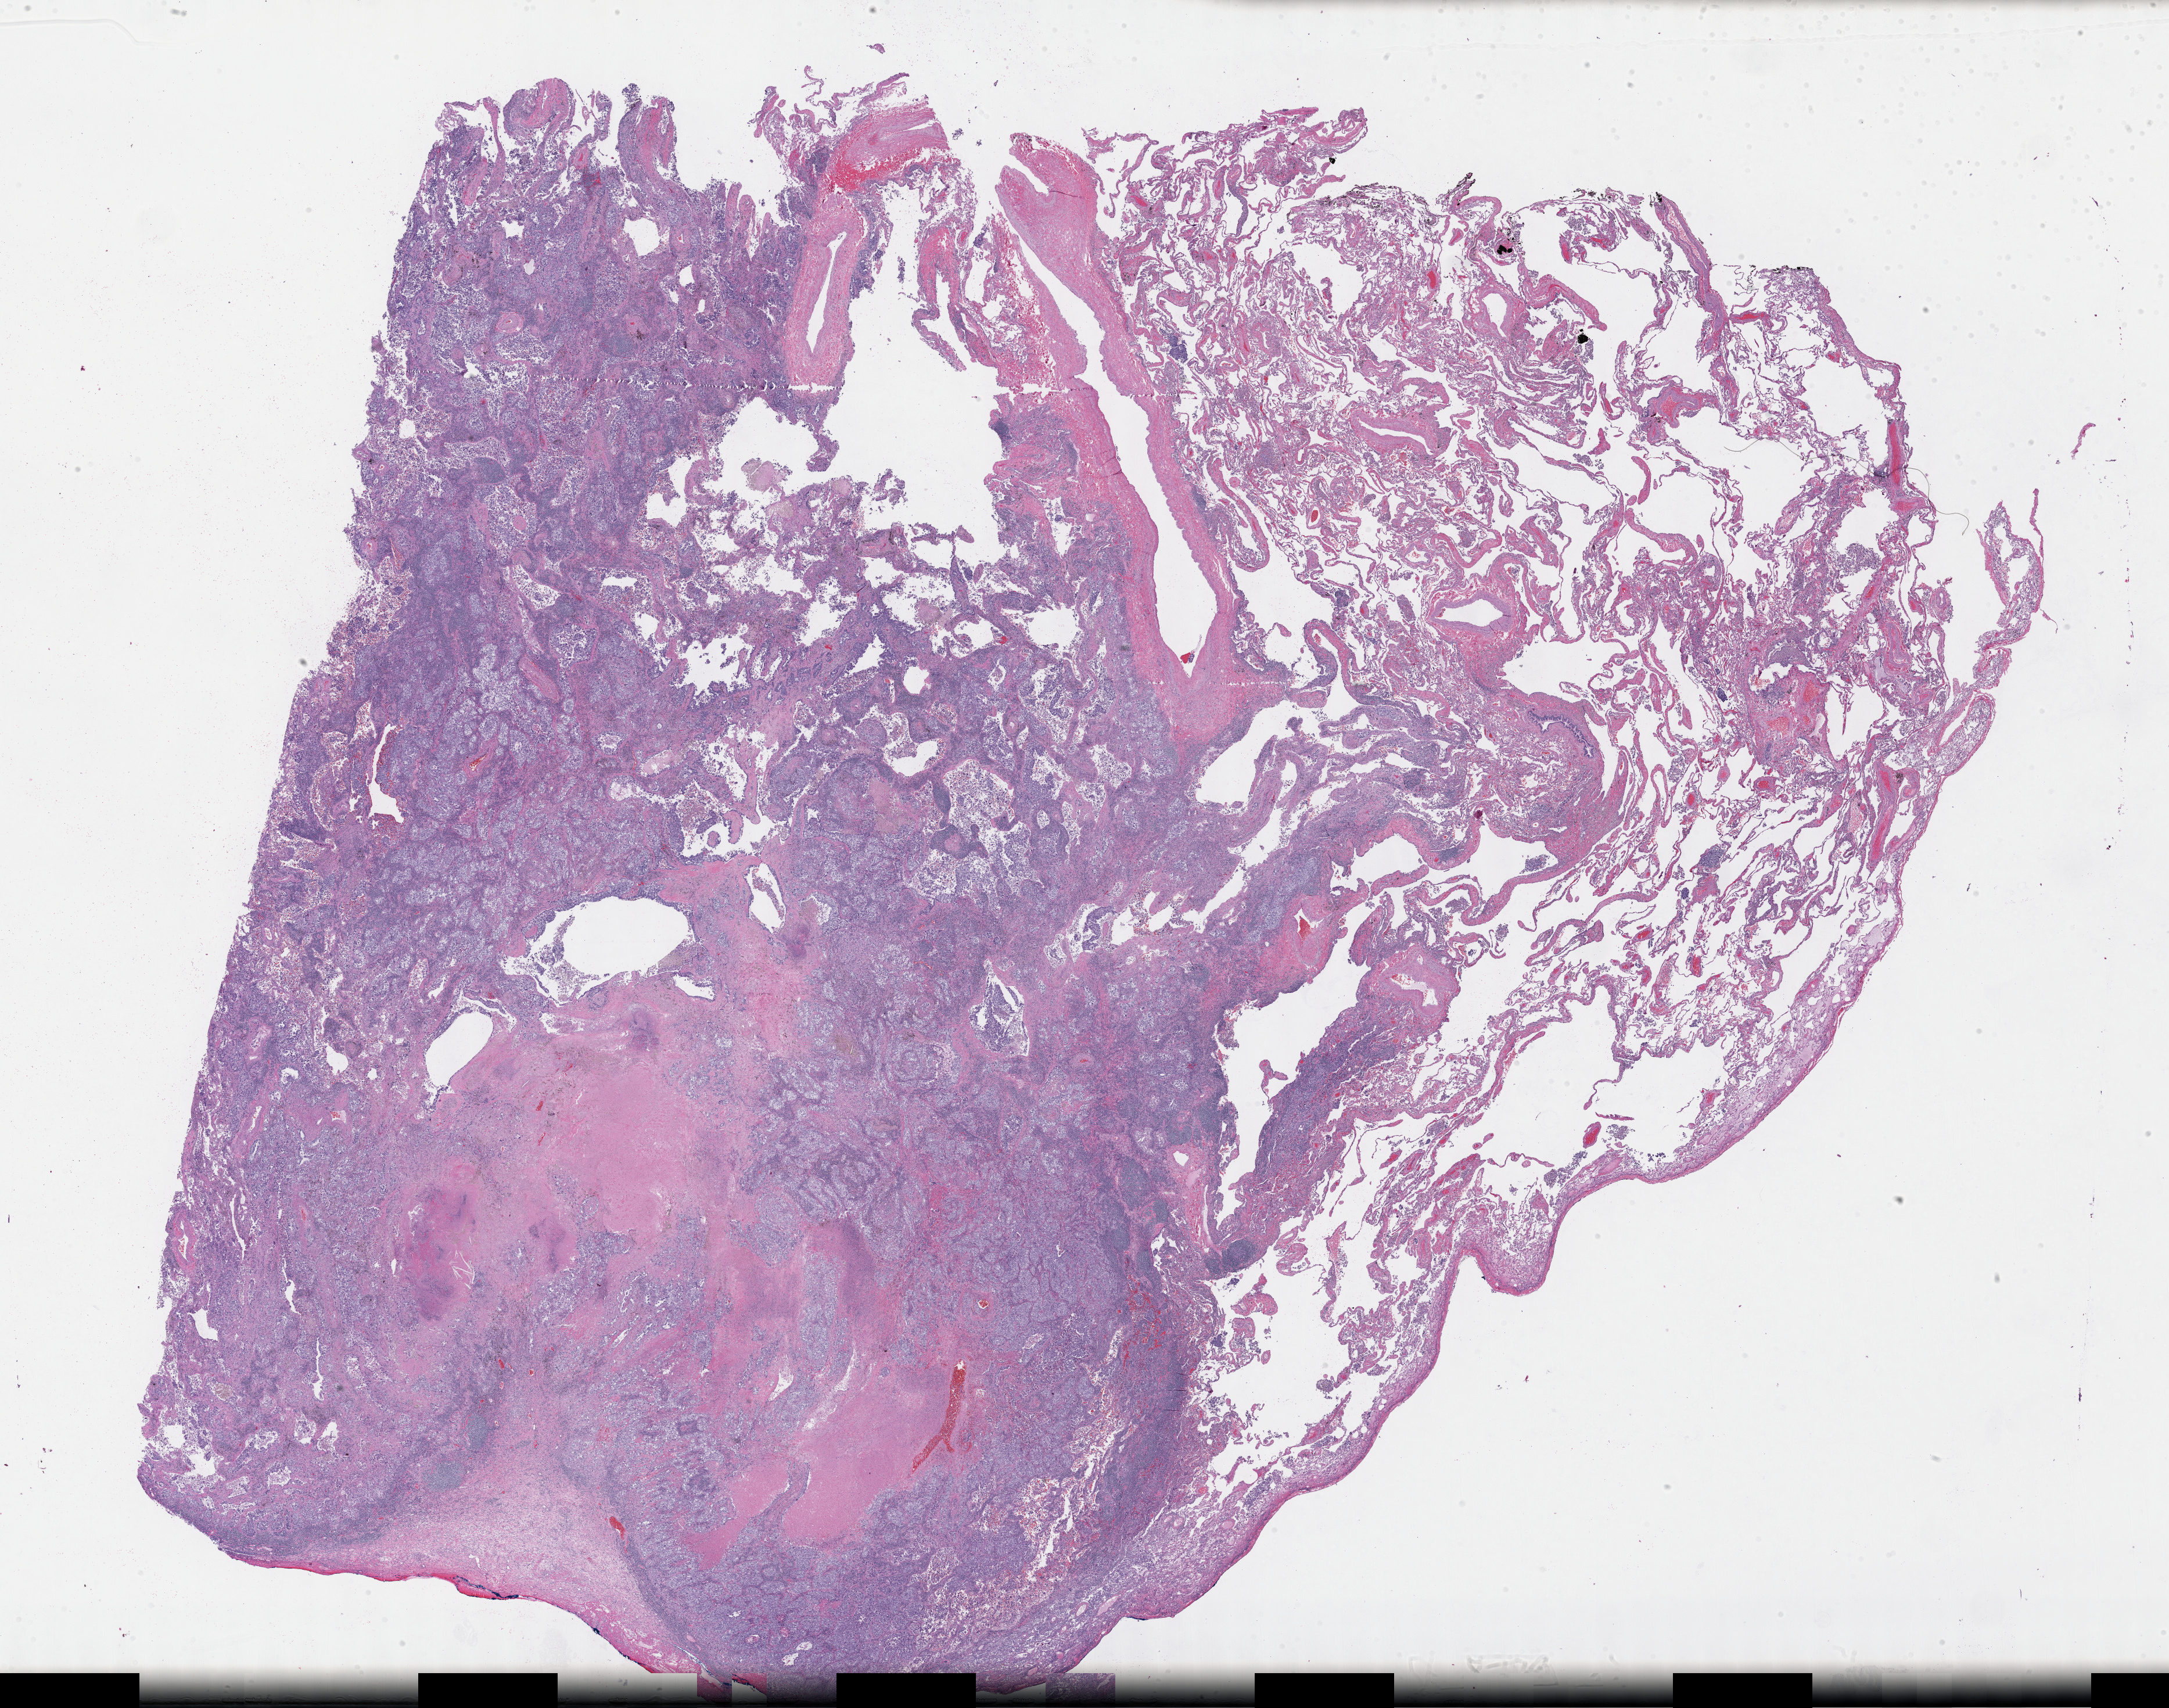
Digitized H&E-stained tissue section (whole slide), low-resolution overview of the scanned area, about 30.2 x 23.8 mm, FFPE section, sample: primary tumour, lung. Female, age 64 years at initial diagnosis.
AJCC pathologic stage: IB. Laterality: left. Pathologic diagnosis: Adenocarcinoma, NOS.